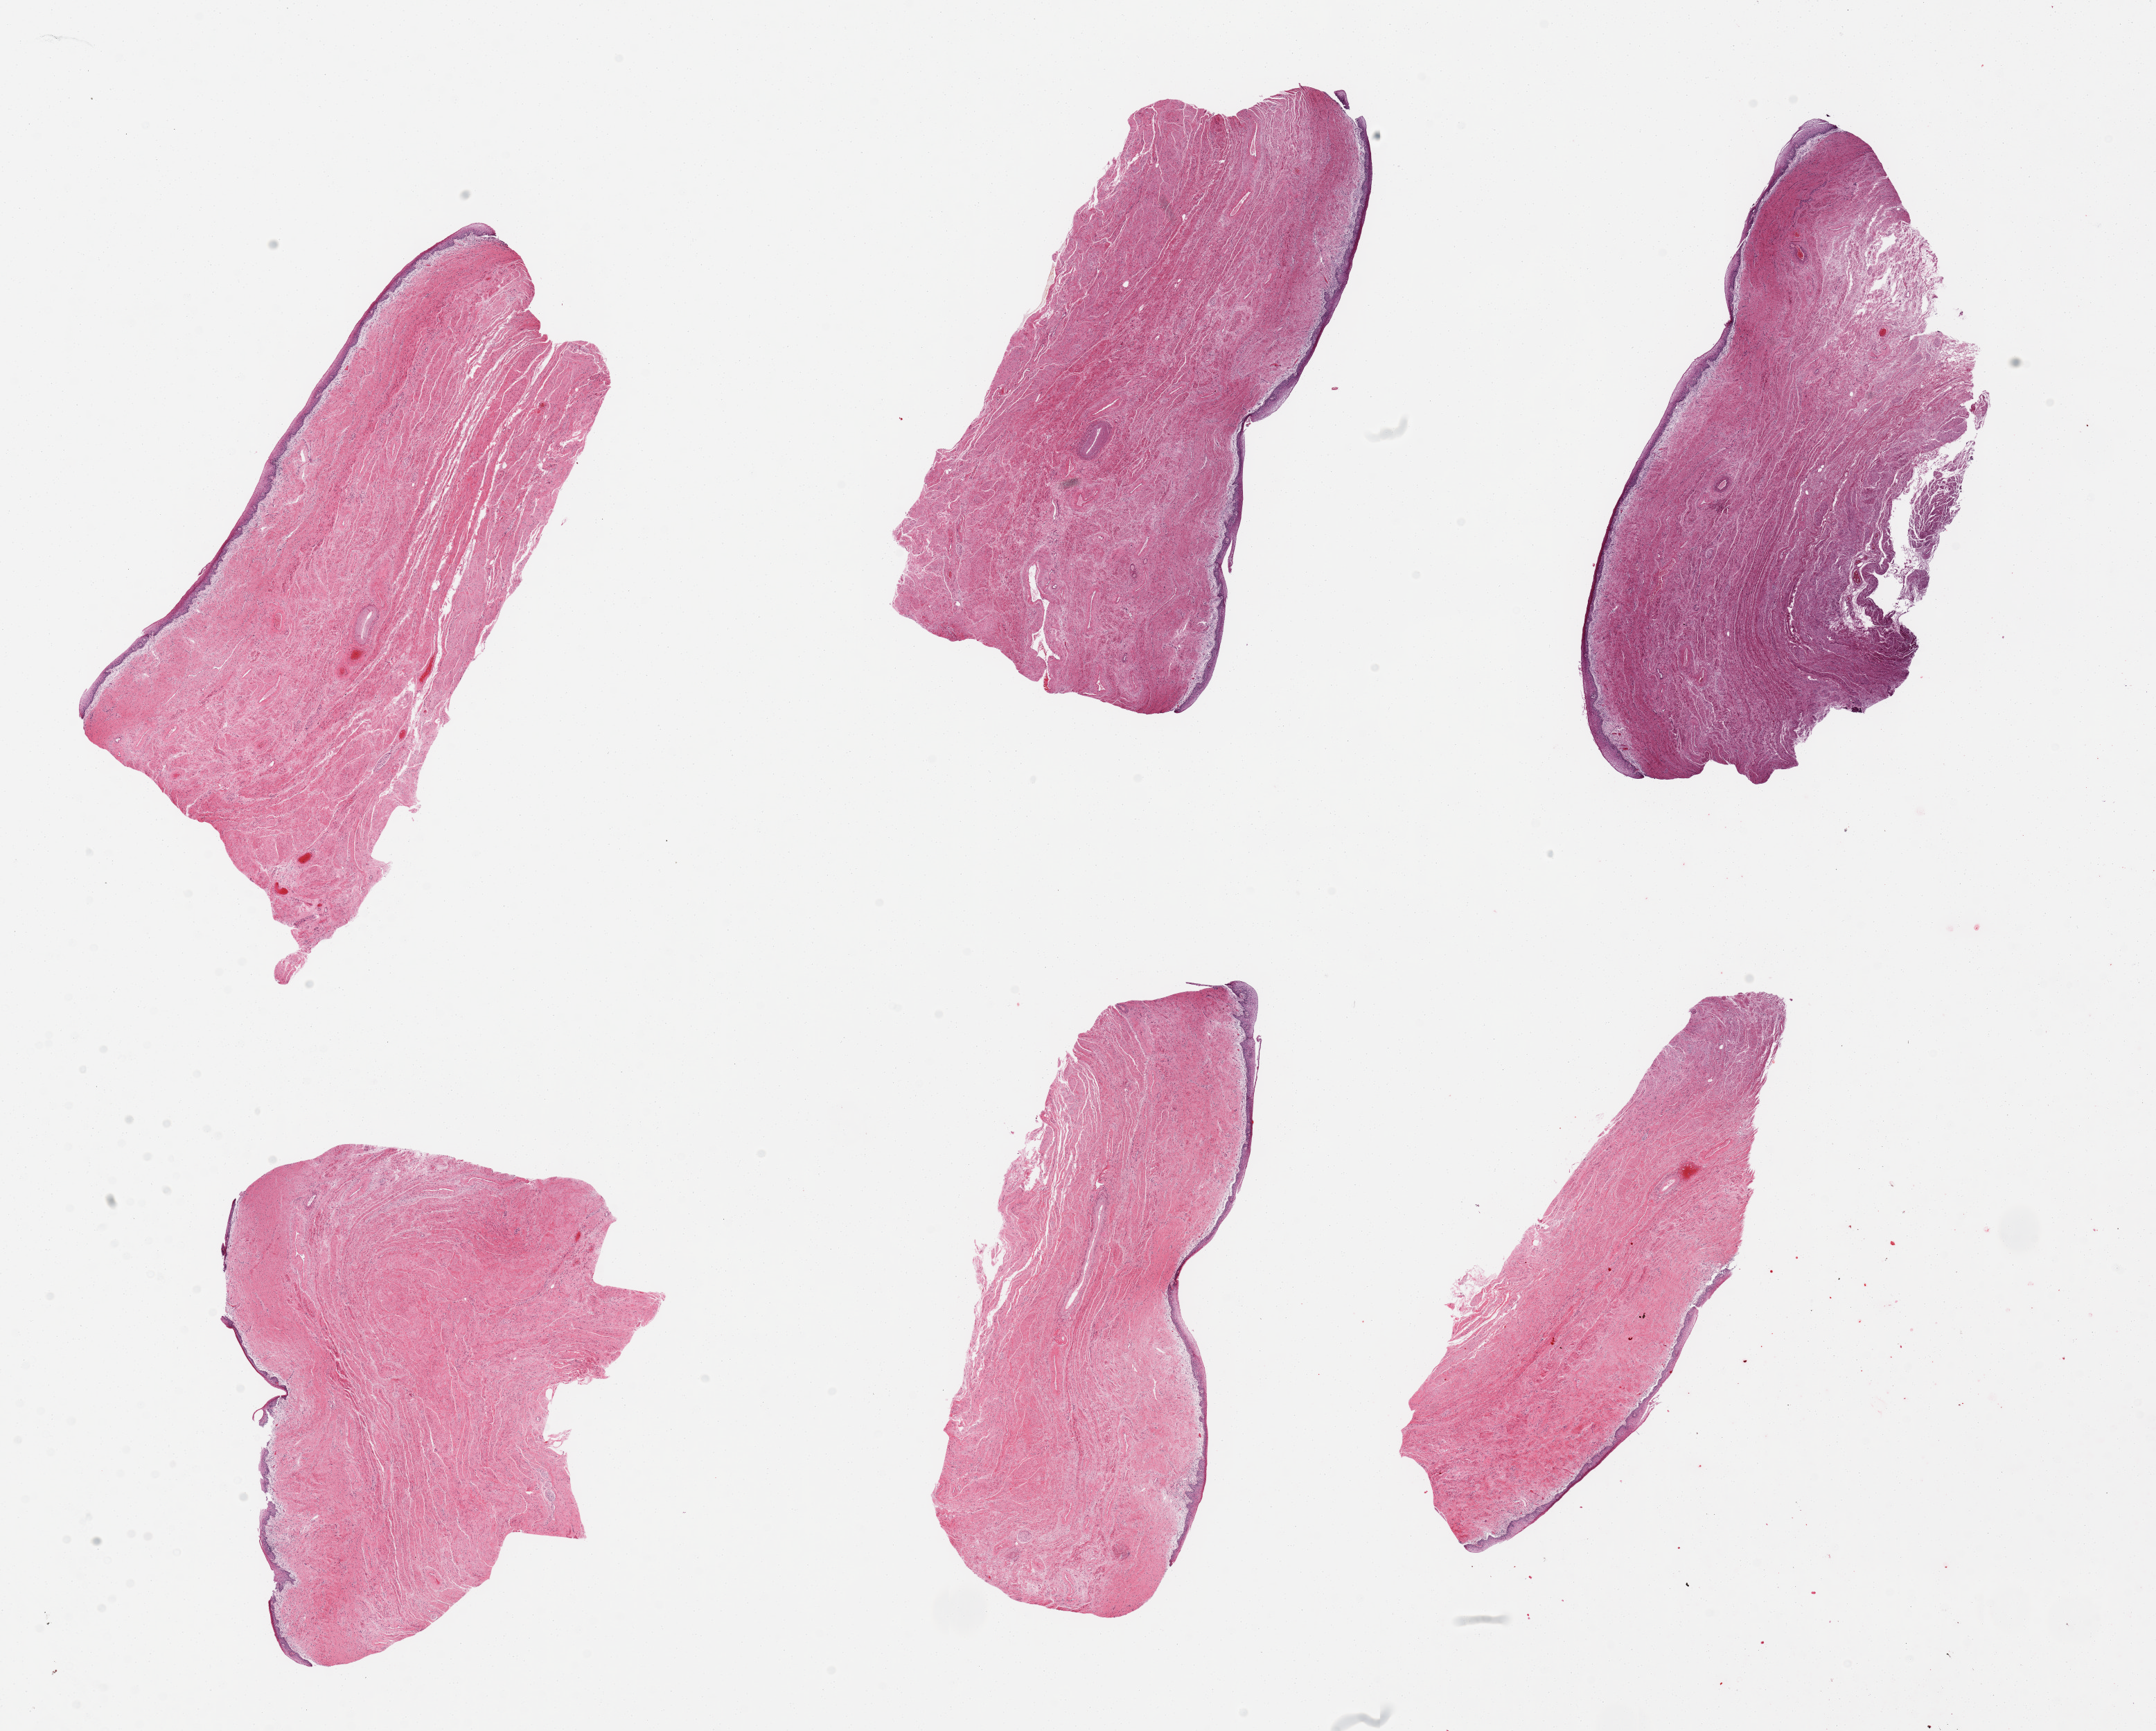
Whole-slide image, hematoxylin and eosin (H&E) stain, brightfield — whole scanned area (about 24.6 x 19.8 mm) shown as a low-resolution overview. PAXgene-fixed, paraffin-embedded tissue. Section of vagina (target tissue). Tissue donor sample. Donor sex: female.
• review note (as recorded): 6 pieces